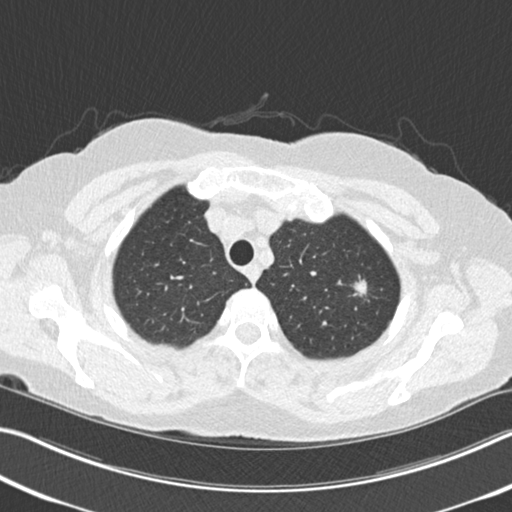
Low-dose screening chest CT, one axial slice; position 191 of 225 along the scan axis; lung window (W 1500 / L -600 HU); 2 mm slice thickness; 512 × 512 image matrix, field of view 342 × 342 mm.
Outlined on this slice (manually delineated by an expert):
- lesion 1 (tumor): bounding box <353,279,367,297> (left, top, right, bottom; pixels)